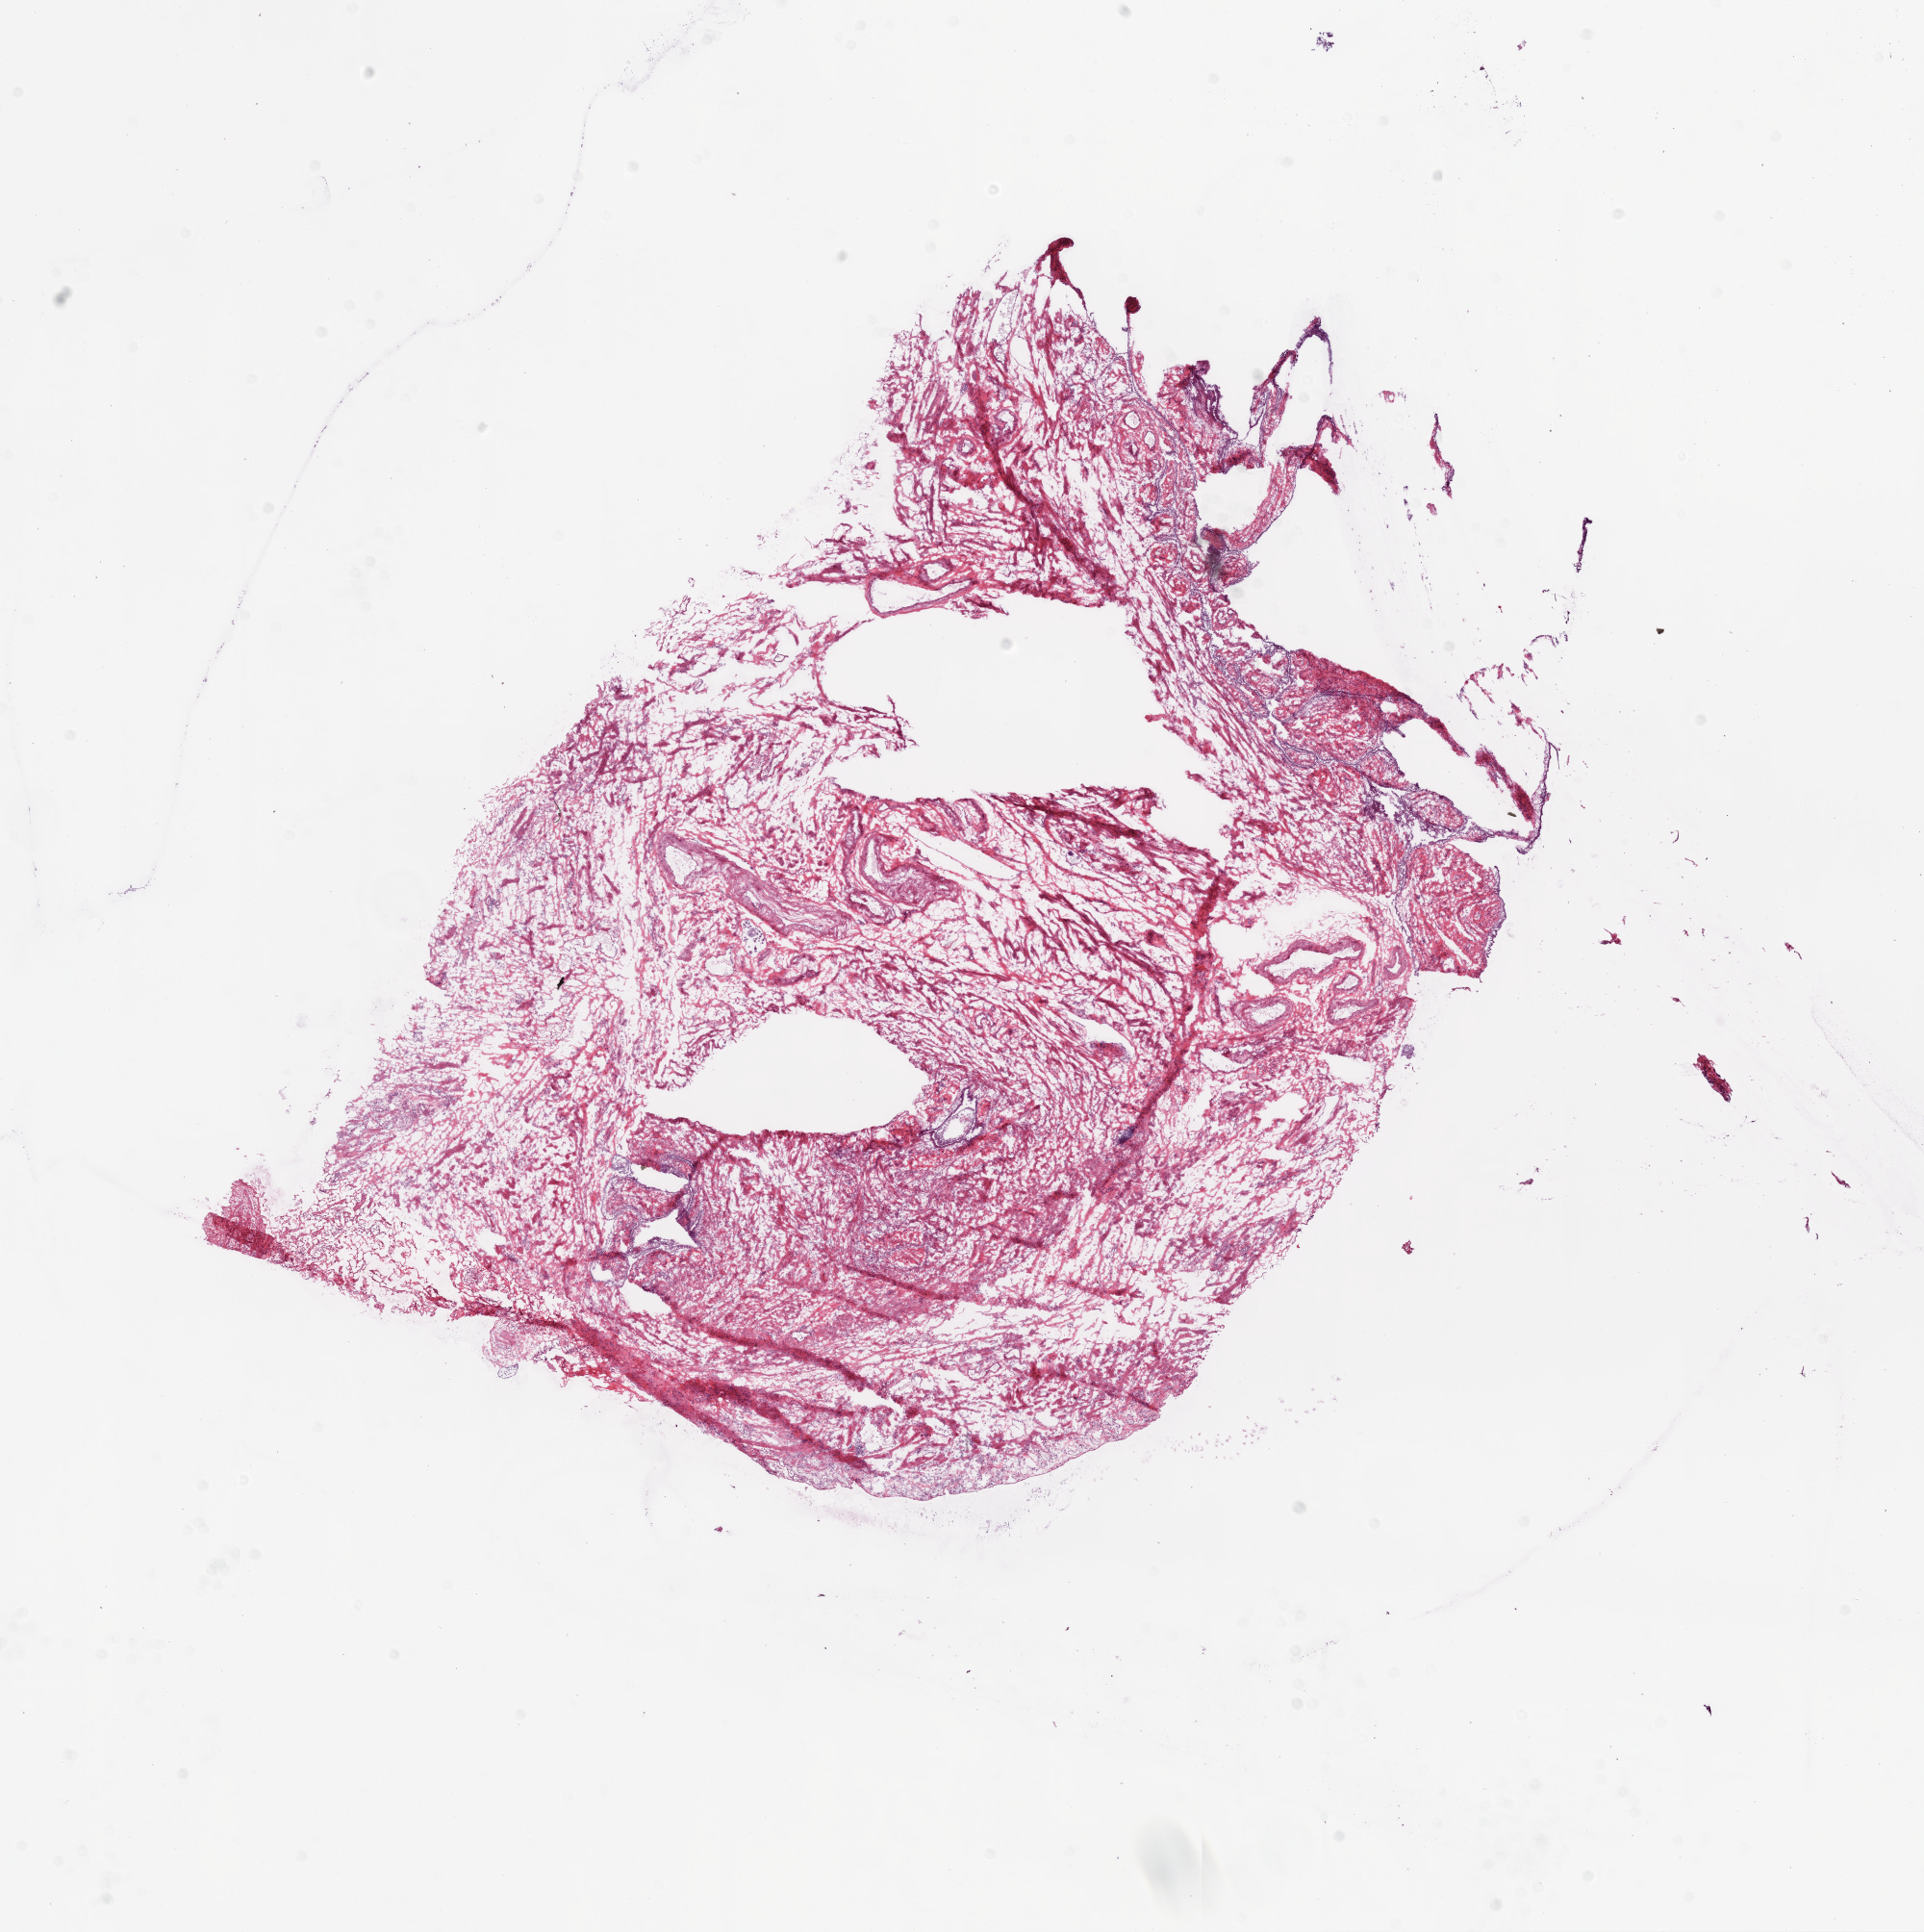
Whole-slide histology image, H&E — shown as a low-resolution overview of the whole scanned area (about 16.0 x 16.1 mm). Frozen section from the bottom of the tissue portion. Ovary, solid tissue normal (non-tumour tissue) sample. Patient: female, age at initial diagnosis 65 years.
- this section: solid tissue normal (non-tumour) sample from the same patient
- patient diagnosis: Serous cystadenocarcinoma, NOS